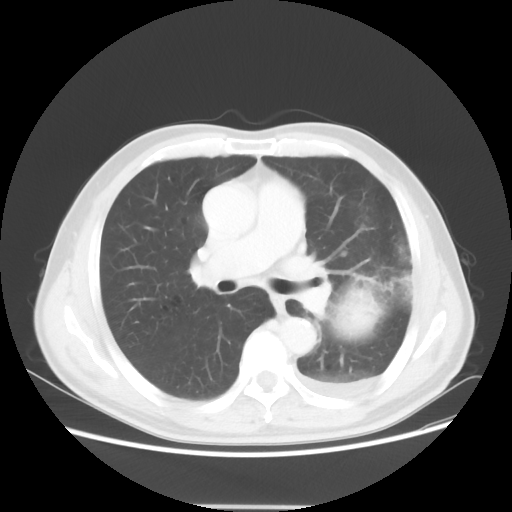
Chest CT, one axial slice. Position 31 of 53 along the scan axis. Reconstruction kernel STANDARD. Lung window (W 1500 / L -600 HU). 5 mm slice thickness. 512 × 512 image matrix, field of view 391 × 391 mm. Male patient, age 60 years. Case-level facts recorded for this patient, not image findings: clinical TNM (as recorded): T4 N1 M1a; histopathological grade: G3.
Structures marked on this image (rectangle marked by the reading radiologist):
- lung tumour (recorded histology: large cell carcinoma): box from (x=337, y=285) to (x=389, y=336) px